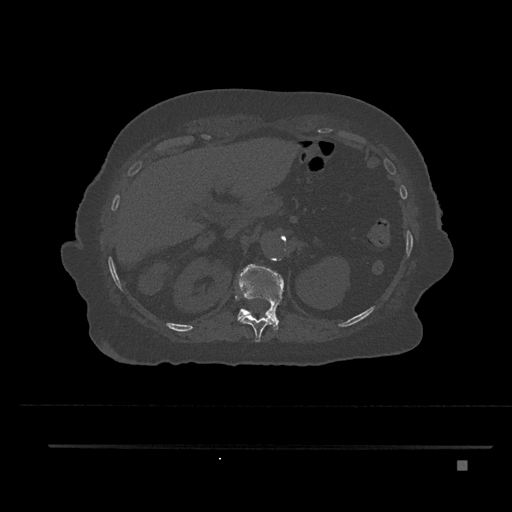
CT including the spine, one axial slice; slice 288 of 797 in the series (ordered by position); reconstruction kernel Br40s/3; 120 kVp; bone window (W 1800 / L 400 HU); 0.5 mm slice thickness; 512 × 512 image matrix. Female patient, age 76 years. From the clinical record (not read from this slice): primary cancer: lung; vertebrae with lytic lesions (as recorded): T11, L3.
Annotated regions visible in this slice (semi-automatically segmented with operator editing):
- T11 vertebra: box from (x=239, y=292) to (x=283, y=342) px
- T12 vertebra: (x=236, y=264)–(x=284, y=330)